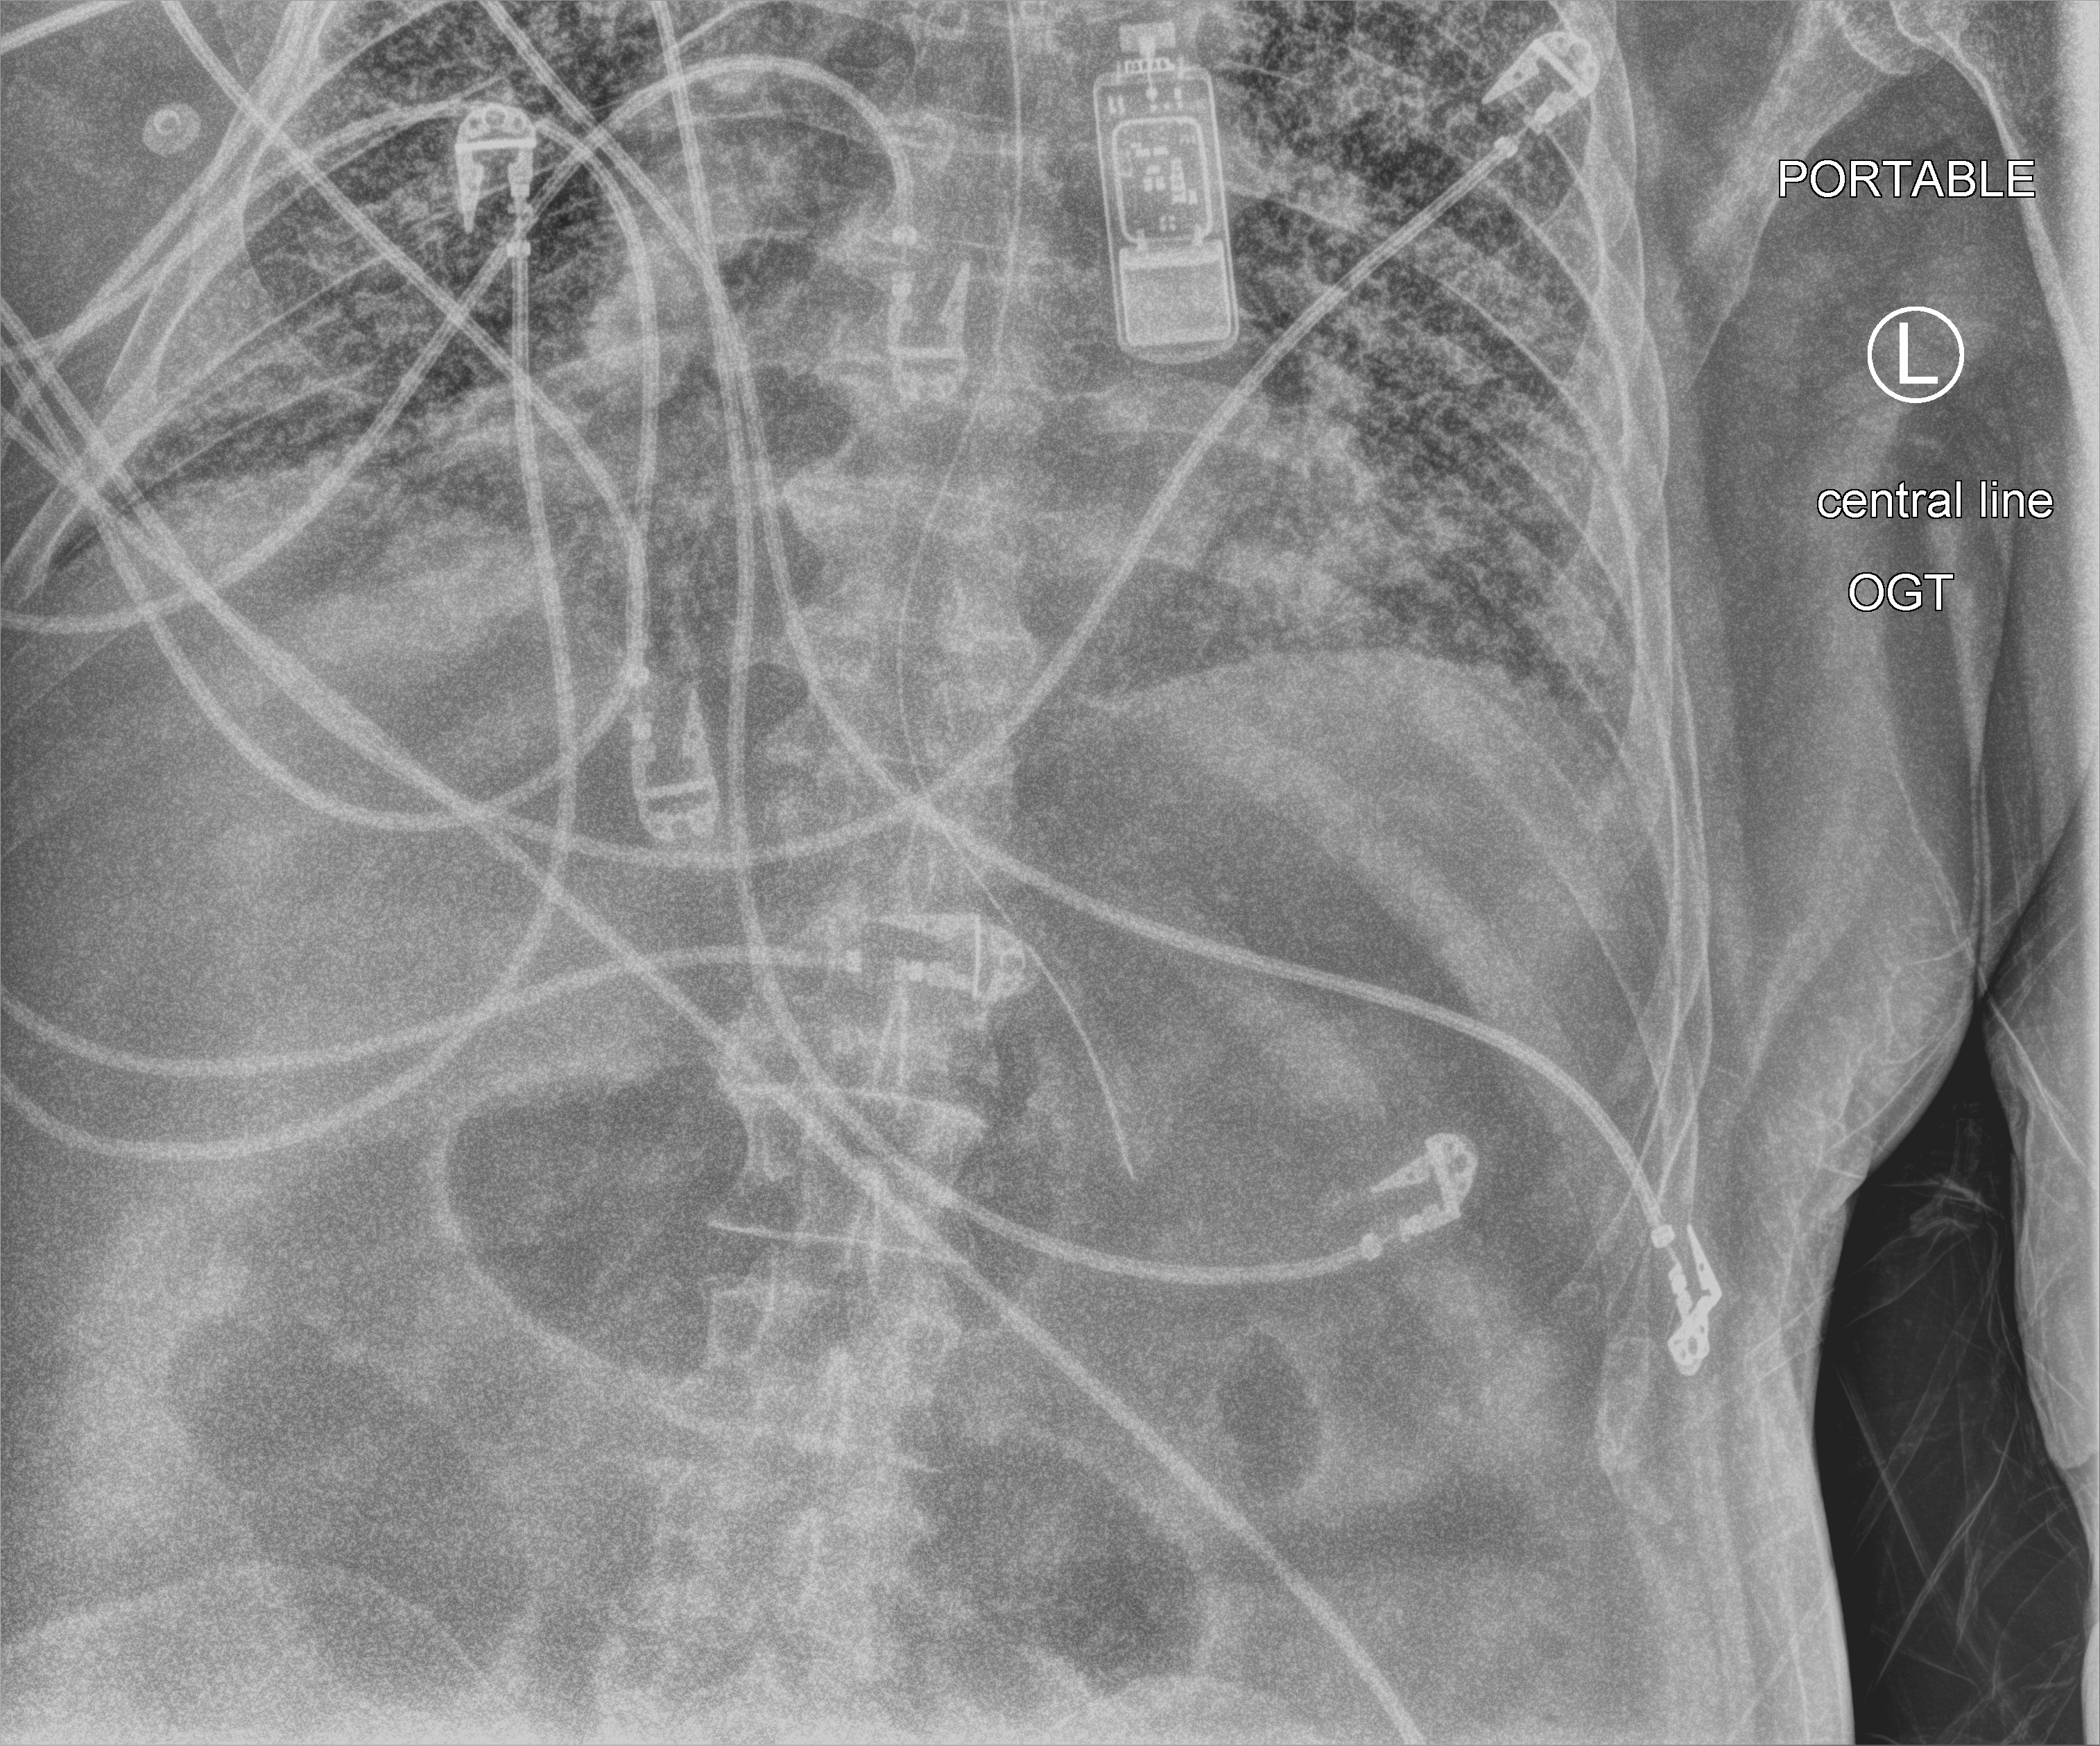
Bedside chest radiograph (computed radiography); anteroposterior (AP) projection. Patient hospitalised with COVID-19; male, aged 60–74 years.
Hospital-stay facts (about this admission, not read from this image; timing relative to this image not recorded):
- mechanically ventilated during this hospital stay: yes
- other chronic lung disease (admission record): yes
- length of hospital stay: 7 days